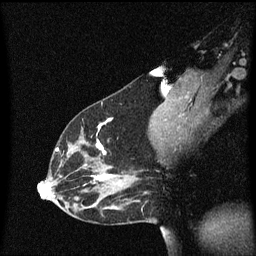
Breast MRI (dynamic contrast-enhanced), one sagittal slice. Position 34 of 60 along the scan axis. Dynamic contrast-enhanced series, image 2 of 3 at this slice position (ordered by acquisition). 1.5 T. TE 4.2 ms, TR 8.4 ms. 2 mm slice thickness. 256 × 256 image matrix, field of view 200 × 200 mm. Patient: female, 33 years.
Annotated regions visible in this slice (semi-automatic segmentation, software-assisted and operator-edited):
- analysis volume of interest (the breast-tissue region the enhancement analysis was run in; not a lesion): box from (x=45, y=116) to (x=152, y=191) px
- tumour enhancement mask (voxels above the 70 % enhancement threshold inside the analysis volume of interest): (x=57, y=118)–(x=115, y=187)